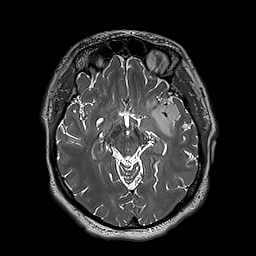
Brain MRI from a brain-tumour surgery series, one axial slice; 256 × 256 image matrix. From the clinical record (not read from this slice): histopathology: Astrocytoma; WHO grade: 3; IDH mutation: yes; tumour location: Left Insular.
Structures marked on this image (expert manual segmentation):
- tumour: box from (x=149, y=99) to (x=180, y=138) px